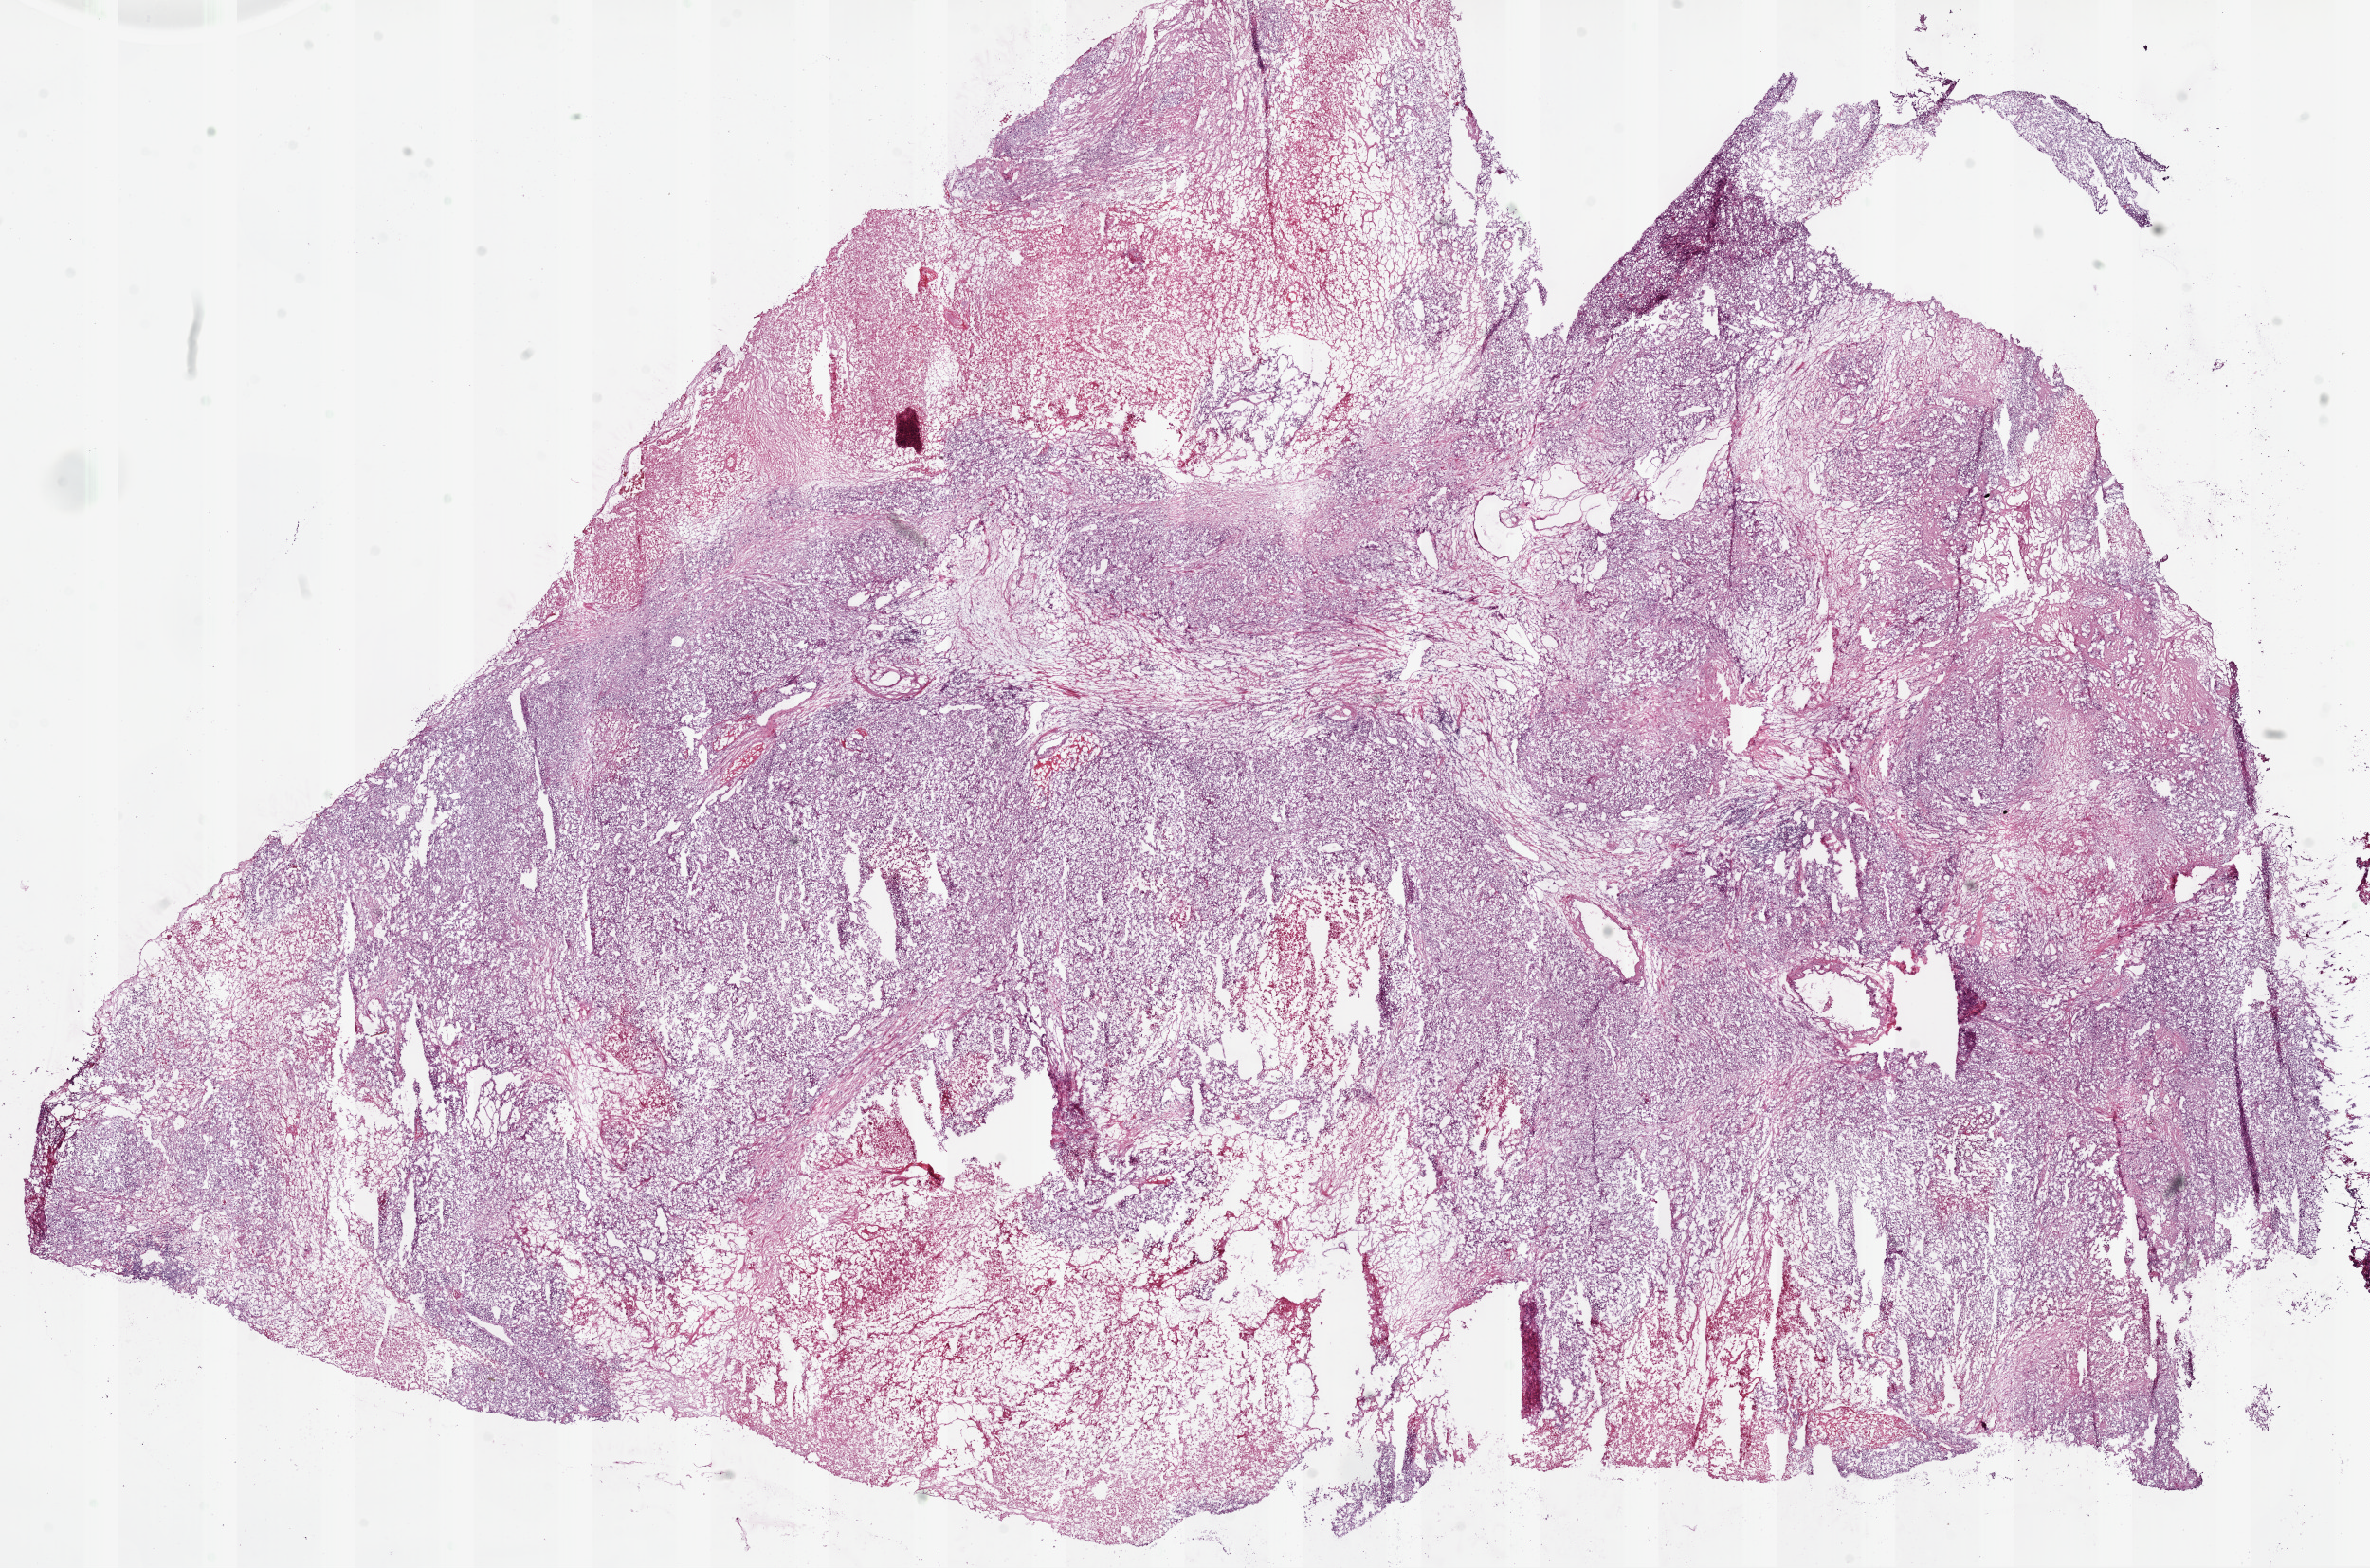
H&E whole-slide image — low-resolution overview of the scanned area, about 20.1 x 13.3 mm (acquisition: 20x scan); frozen section from the bottom of the tissue portion; kidney, primary tumour sample. Male patient; age at initial diagnosis 76 years. Histologic grade: G3 (poorly differentiated). Pathologist review of this section (percent, as recorded): tumour cells 55%, tumour nuclei 80%, normal cells 0%, stromal cells 25%, necrosis 20%.
- AJCC pathologic stage: IV
- histologic diagnosis: Clear cell adenocarcinoma, NOS